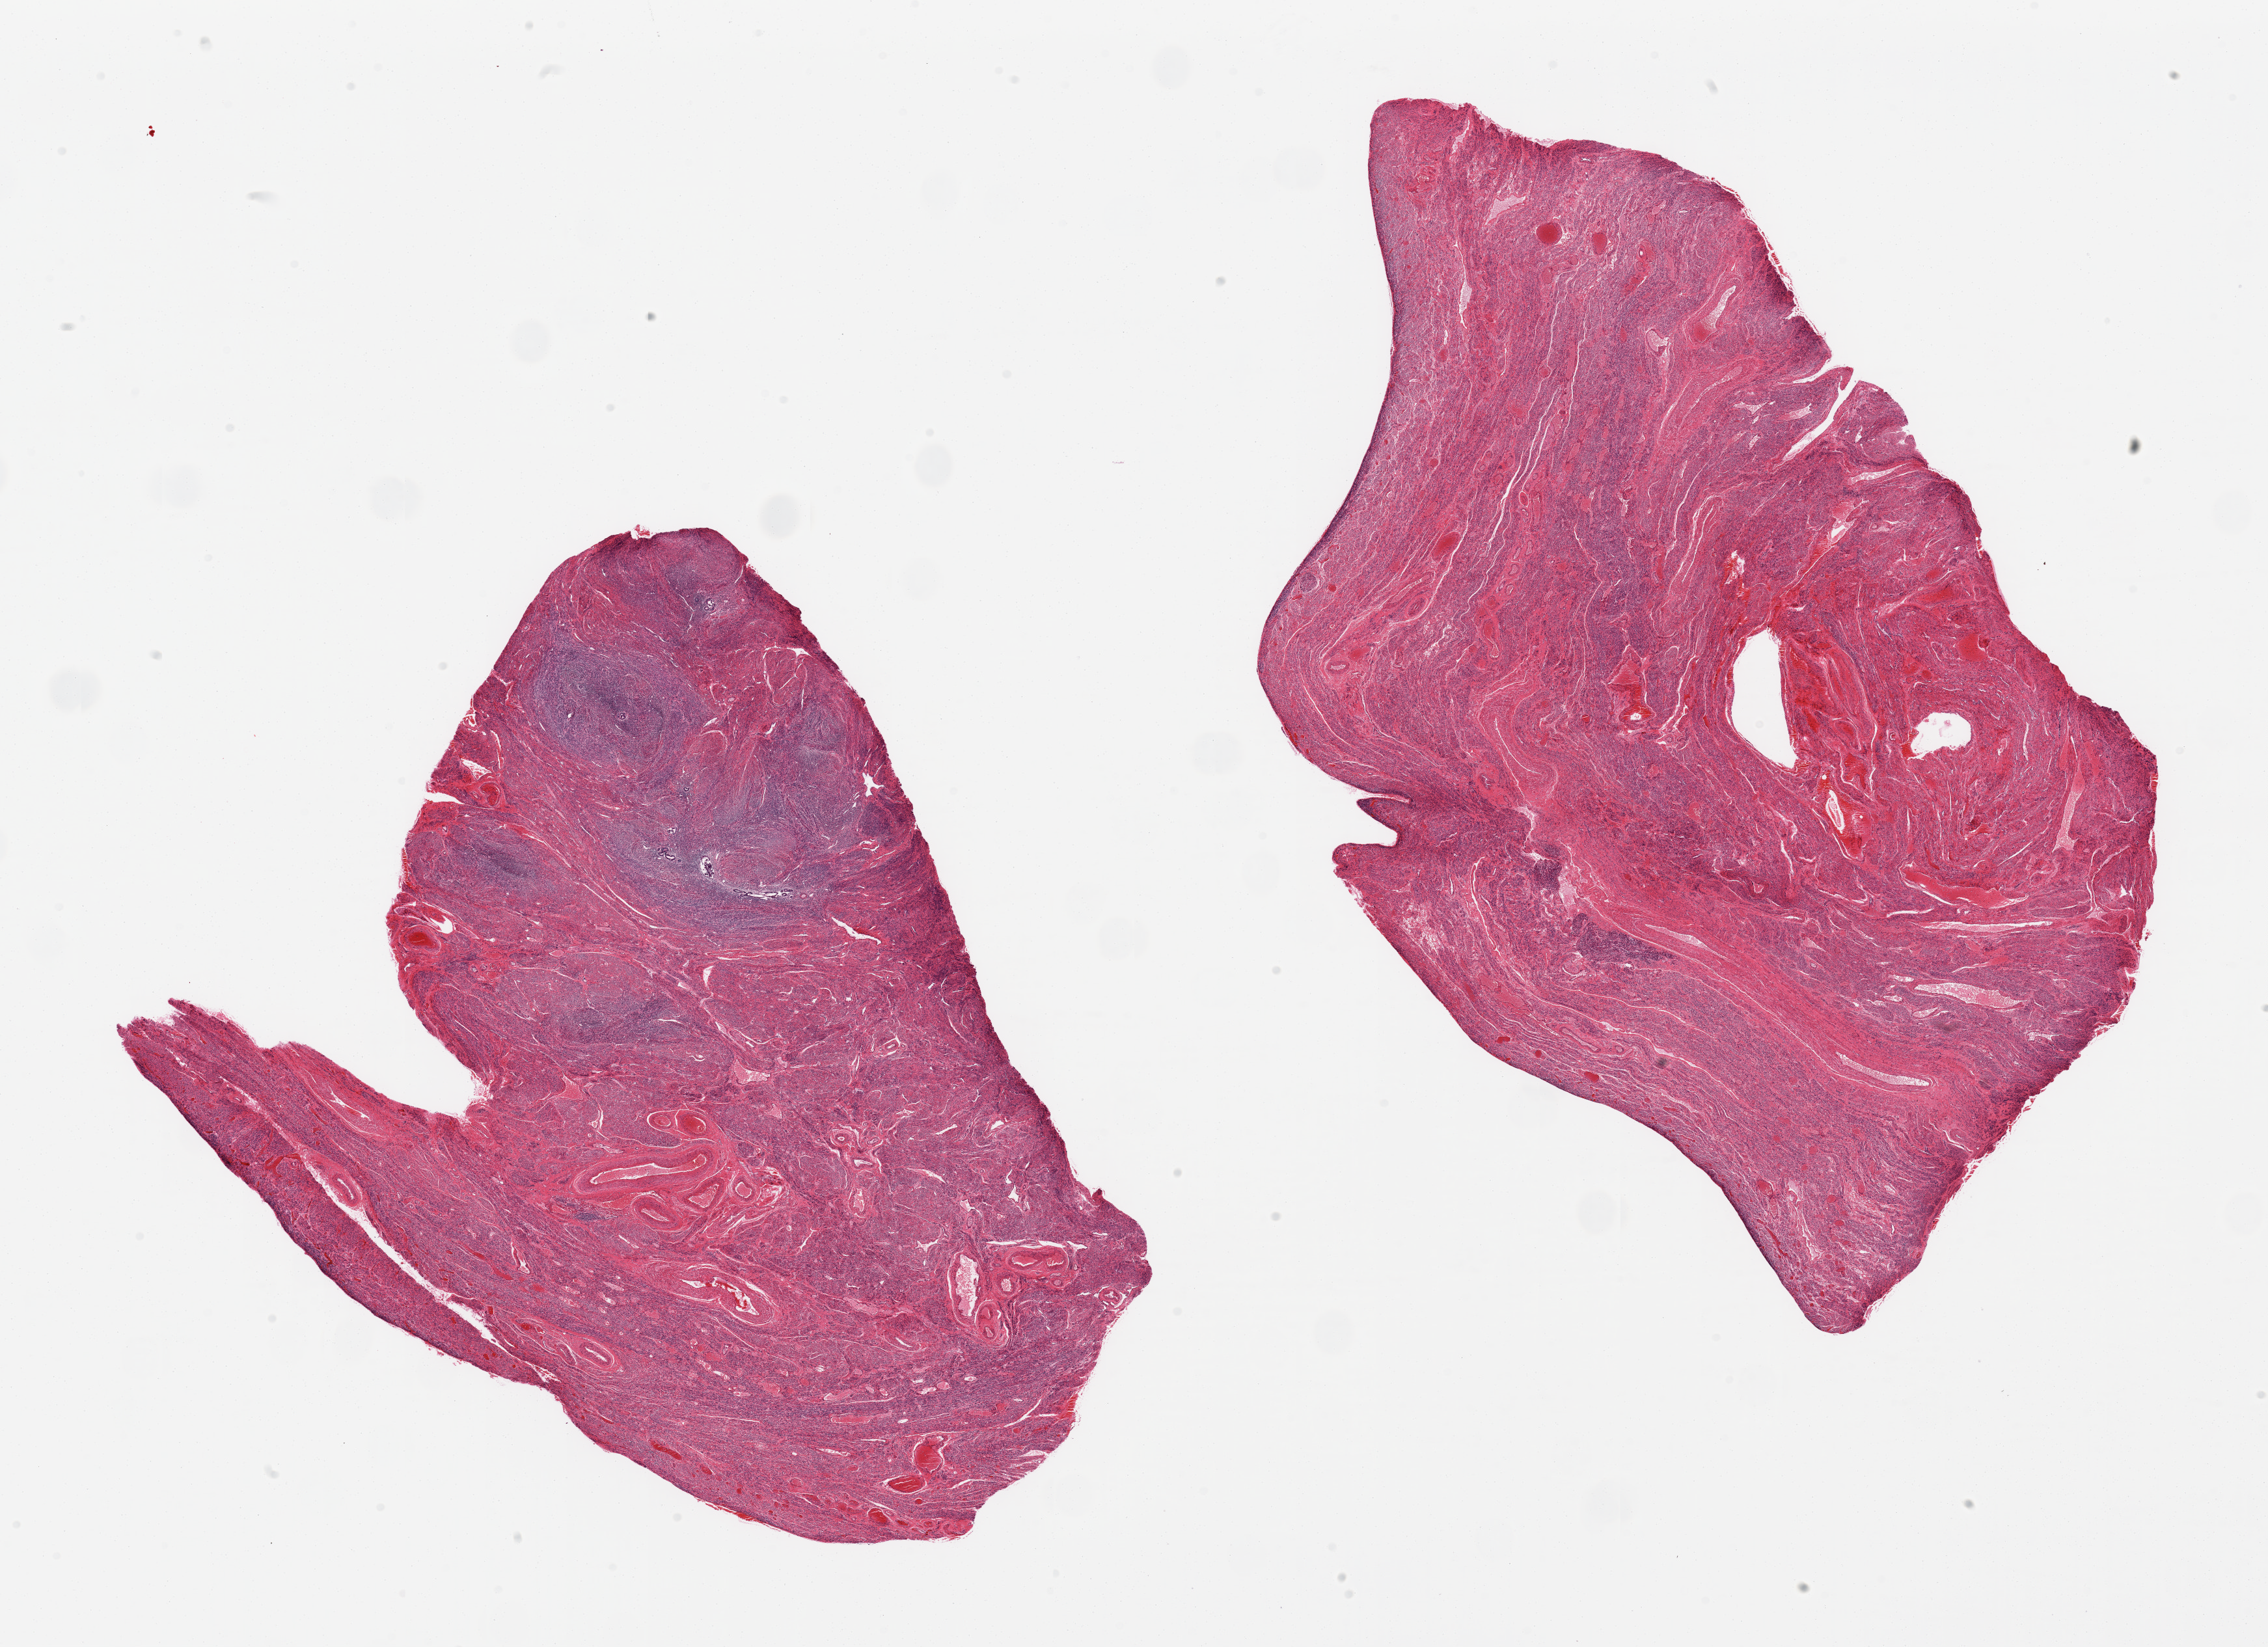
Digitized haematoxylin and eosin-stained section, shown as a low-resolution overview of the whole scanned area (about 27.6 x 20.0 mm); PAXgene-fixed, paraffin-embedded tissue; sampled site (target tissue): uterus; tissue donor sample.
- reviewer comment on this tissue sample: 2 pieces; atrophic endometrium